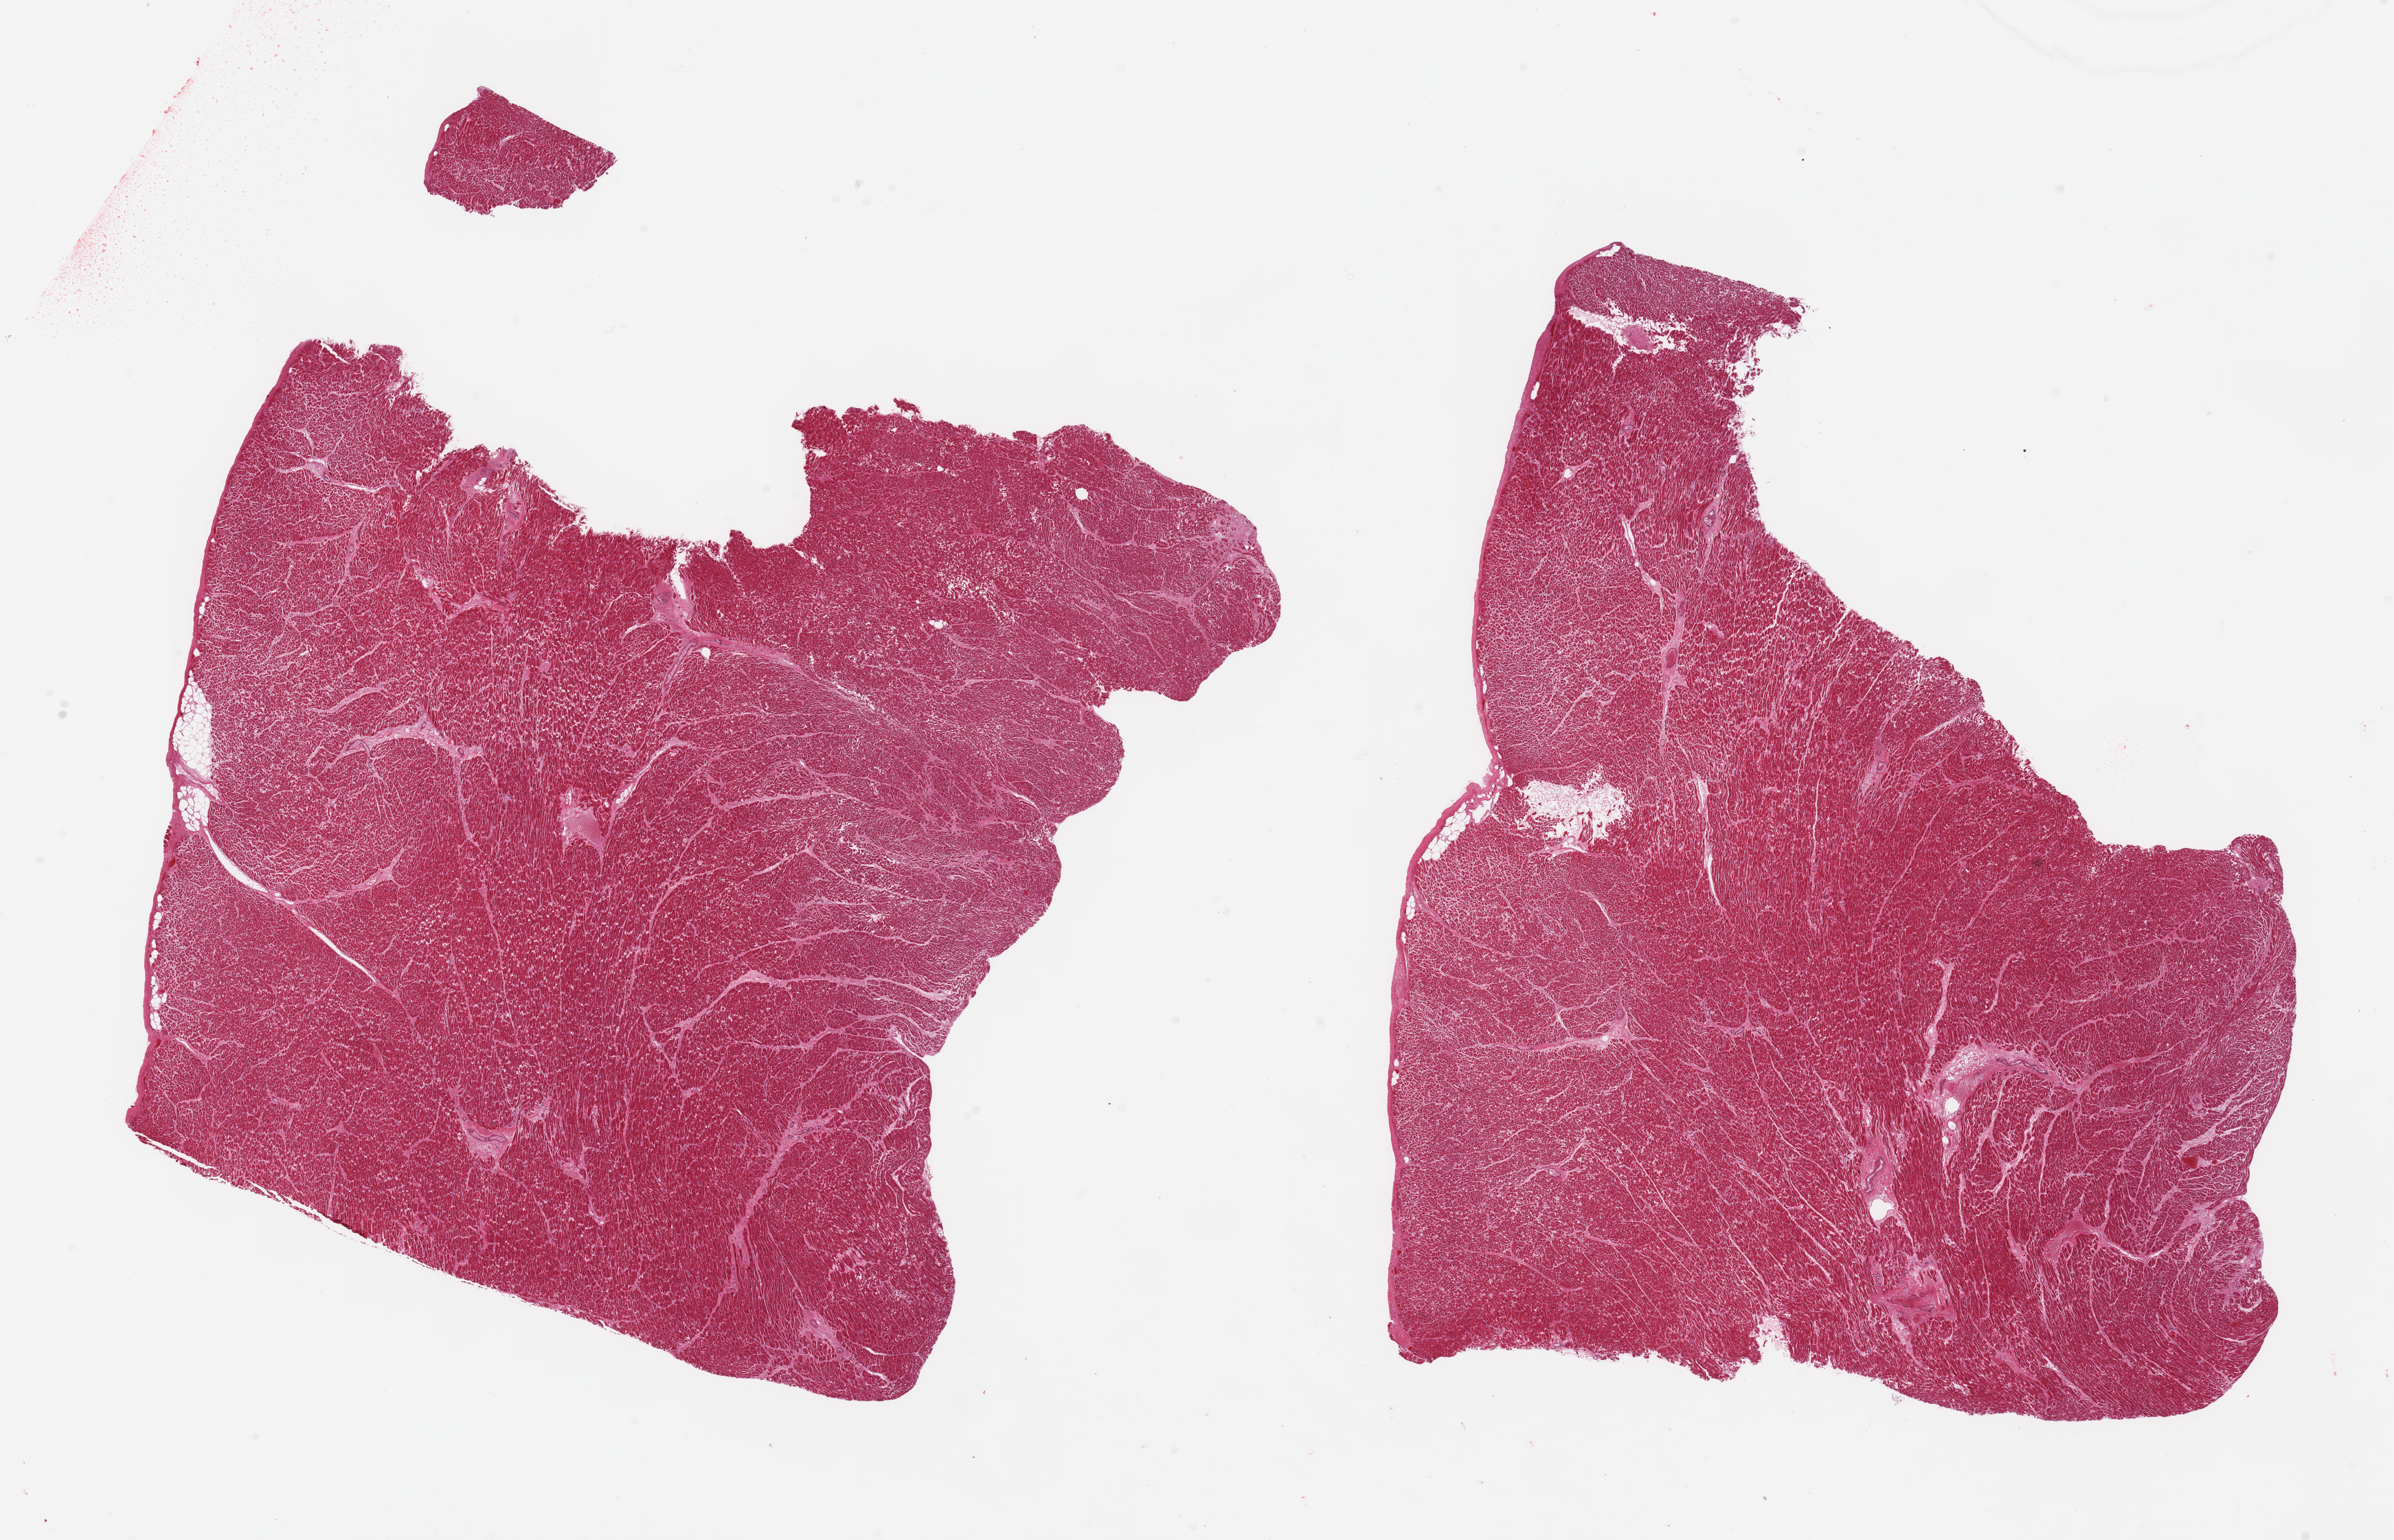
Hematoxylin and eosin (H&E) whole-slide image — low-resolution overview of the scanned area, about 27.6 x 17.7 mm; PAXgene-fixed, paraffin-embedded tissue; section of heart (target tissue); donor tissue sample. Donor: male.
- pathologist's review note for this sample: 2 pieces, moderate interstitial fibrosis/chronic ischemic changes